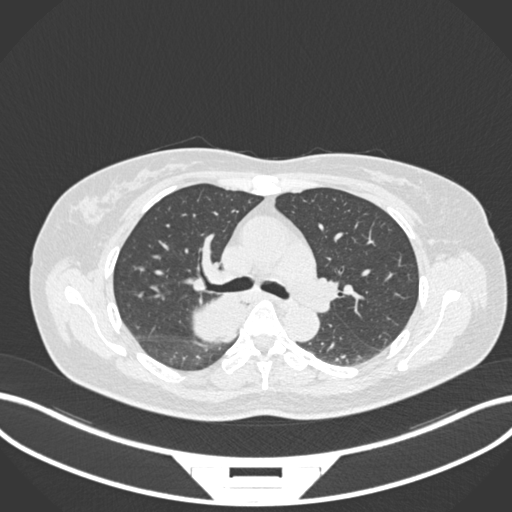
Chest CT, one axial slice; slice 619 of 677 in the series (ordered by position); reconstruction kernel B30f; 120 kVp; lung window (W 1500 / L -600 HU); 1 mm slice thickness; 512 × 512 image matrix. Female patient, age 54 years. Case-level facts recorded for this patient, not image findings: clinical TNM (as recorded): T4 N0 M0.
Outlined on this slice (bounding box drawn by a radiologist):
- lung tumour (recorded histology: adenocarcinoma): bounding box (x1, y1, x2, y2) in pixels: (190, 290, 248, 346)